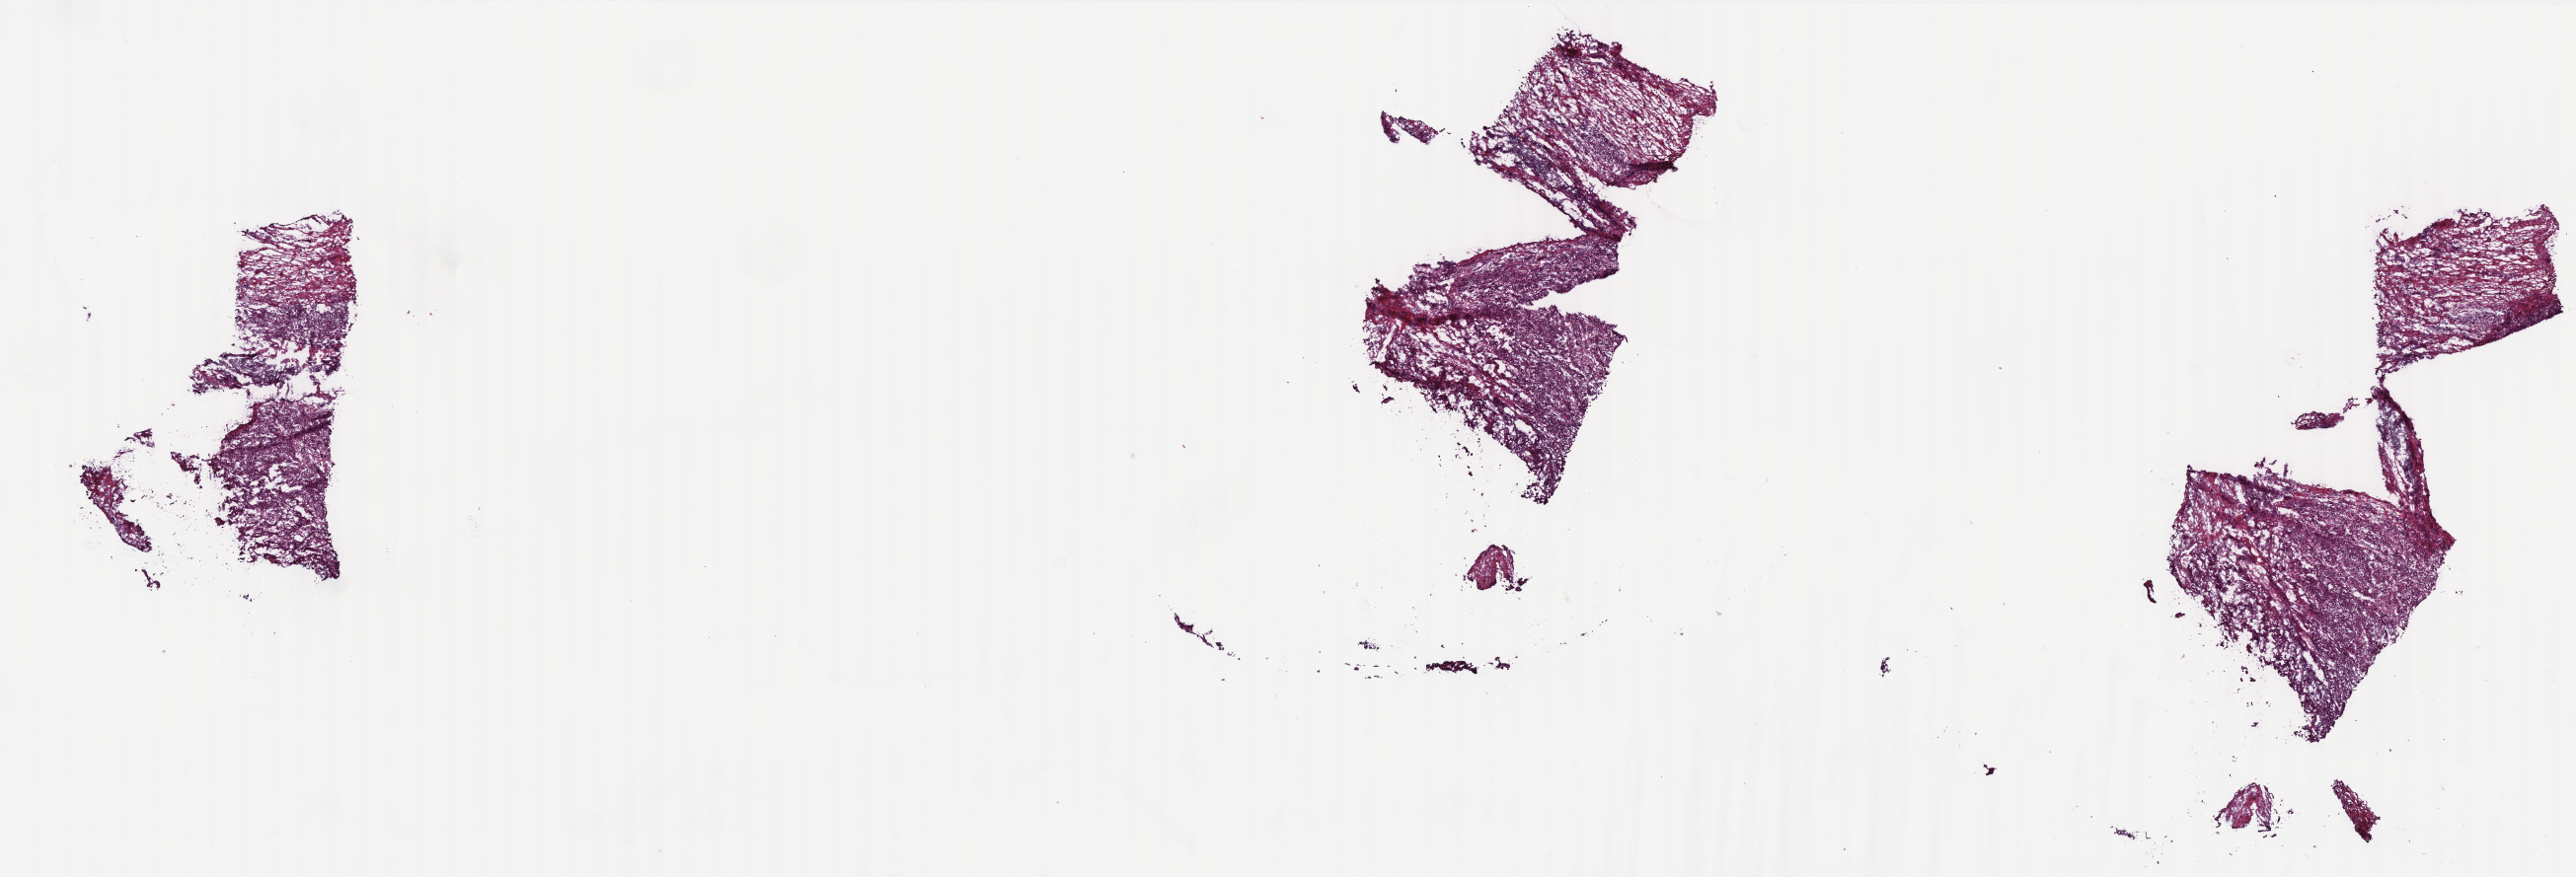
Digitized H&E-stained tissue section (whole slide), shown as a low-resolution overview of the whole scanned area (about 20.9 x 7.1 mm, slide scanned at 40x); frozen section; colon, primary tumour sample. Patient: female, age at initial diagnosis 80 years. Slide review estimates, as recorded: tumour cells 60%, tumour nuclei 65%, normal cells 0%, stromal cells 38%, necrosis 2%. Infiltration values recorded for this section: lymphocyte infiltration 12%, monocyte infiltration 6%, neutrophil infiltration 12%.
Pathologic diagnosis: Adenocarcinoma, NOS (ascending colon). TNM: T3 N1 M0. AJCC pathologic stage: III (5th edition). Lymph nodes positive (case pathology): 1 of 21 examined.